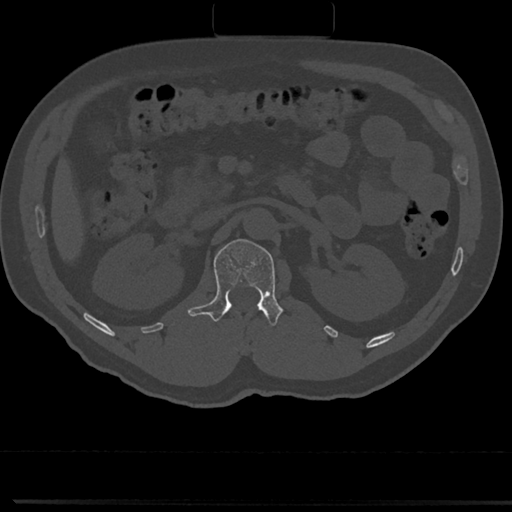
CT including the spine, one axial slice; reconstruction kernel Br40s/3; 120 kVp; bone window (W 1800 / L 400 HU); 0.5 mm slice thickness; 512 × 512 image matrix, field of view 355 × 355 mm. Patient: male, 61 years. Case-level facts recorded for this patient, not image findings: primary cancer: prostate.
Annotated regions visible in this slice (semi-automatically segmented with operator editing):
- L1 vertebra: bounding box (x1, y1, x2, y2) in pixels: (191, 239, 284, 326)